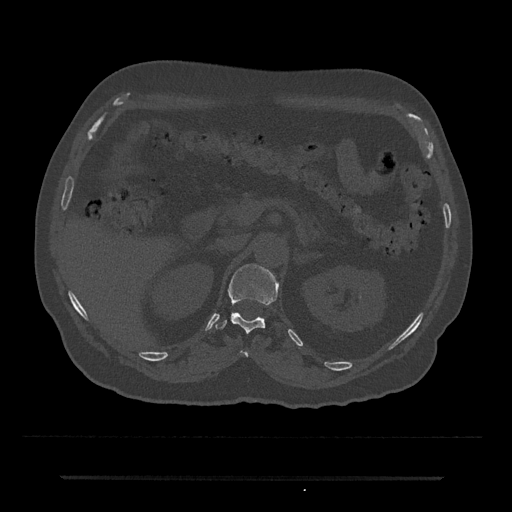
CT including the spine, one axial slice; reconstruction kernel Br40s/3; 120 kVp; bone window (W 1800 / L 400 HU); 0.5 mm slice thickness; 512 × 512 image matrix, field of view 437 × 437 mm. Patient: male, 69 years. Case-level facts recorded for this patient, not image findings: primary cancer: prostate.
Annotated regions visible in this slice (semi-automatic segmentation, software-assisted and operator-edited):
- T11 vertebra: box from (x=241, y=351) to (x=249, y=357) px
- T12 vertebra: (x=215, y=264)–(x=278, y=333)